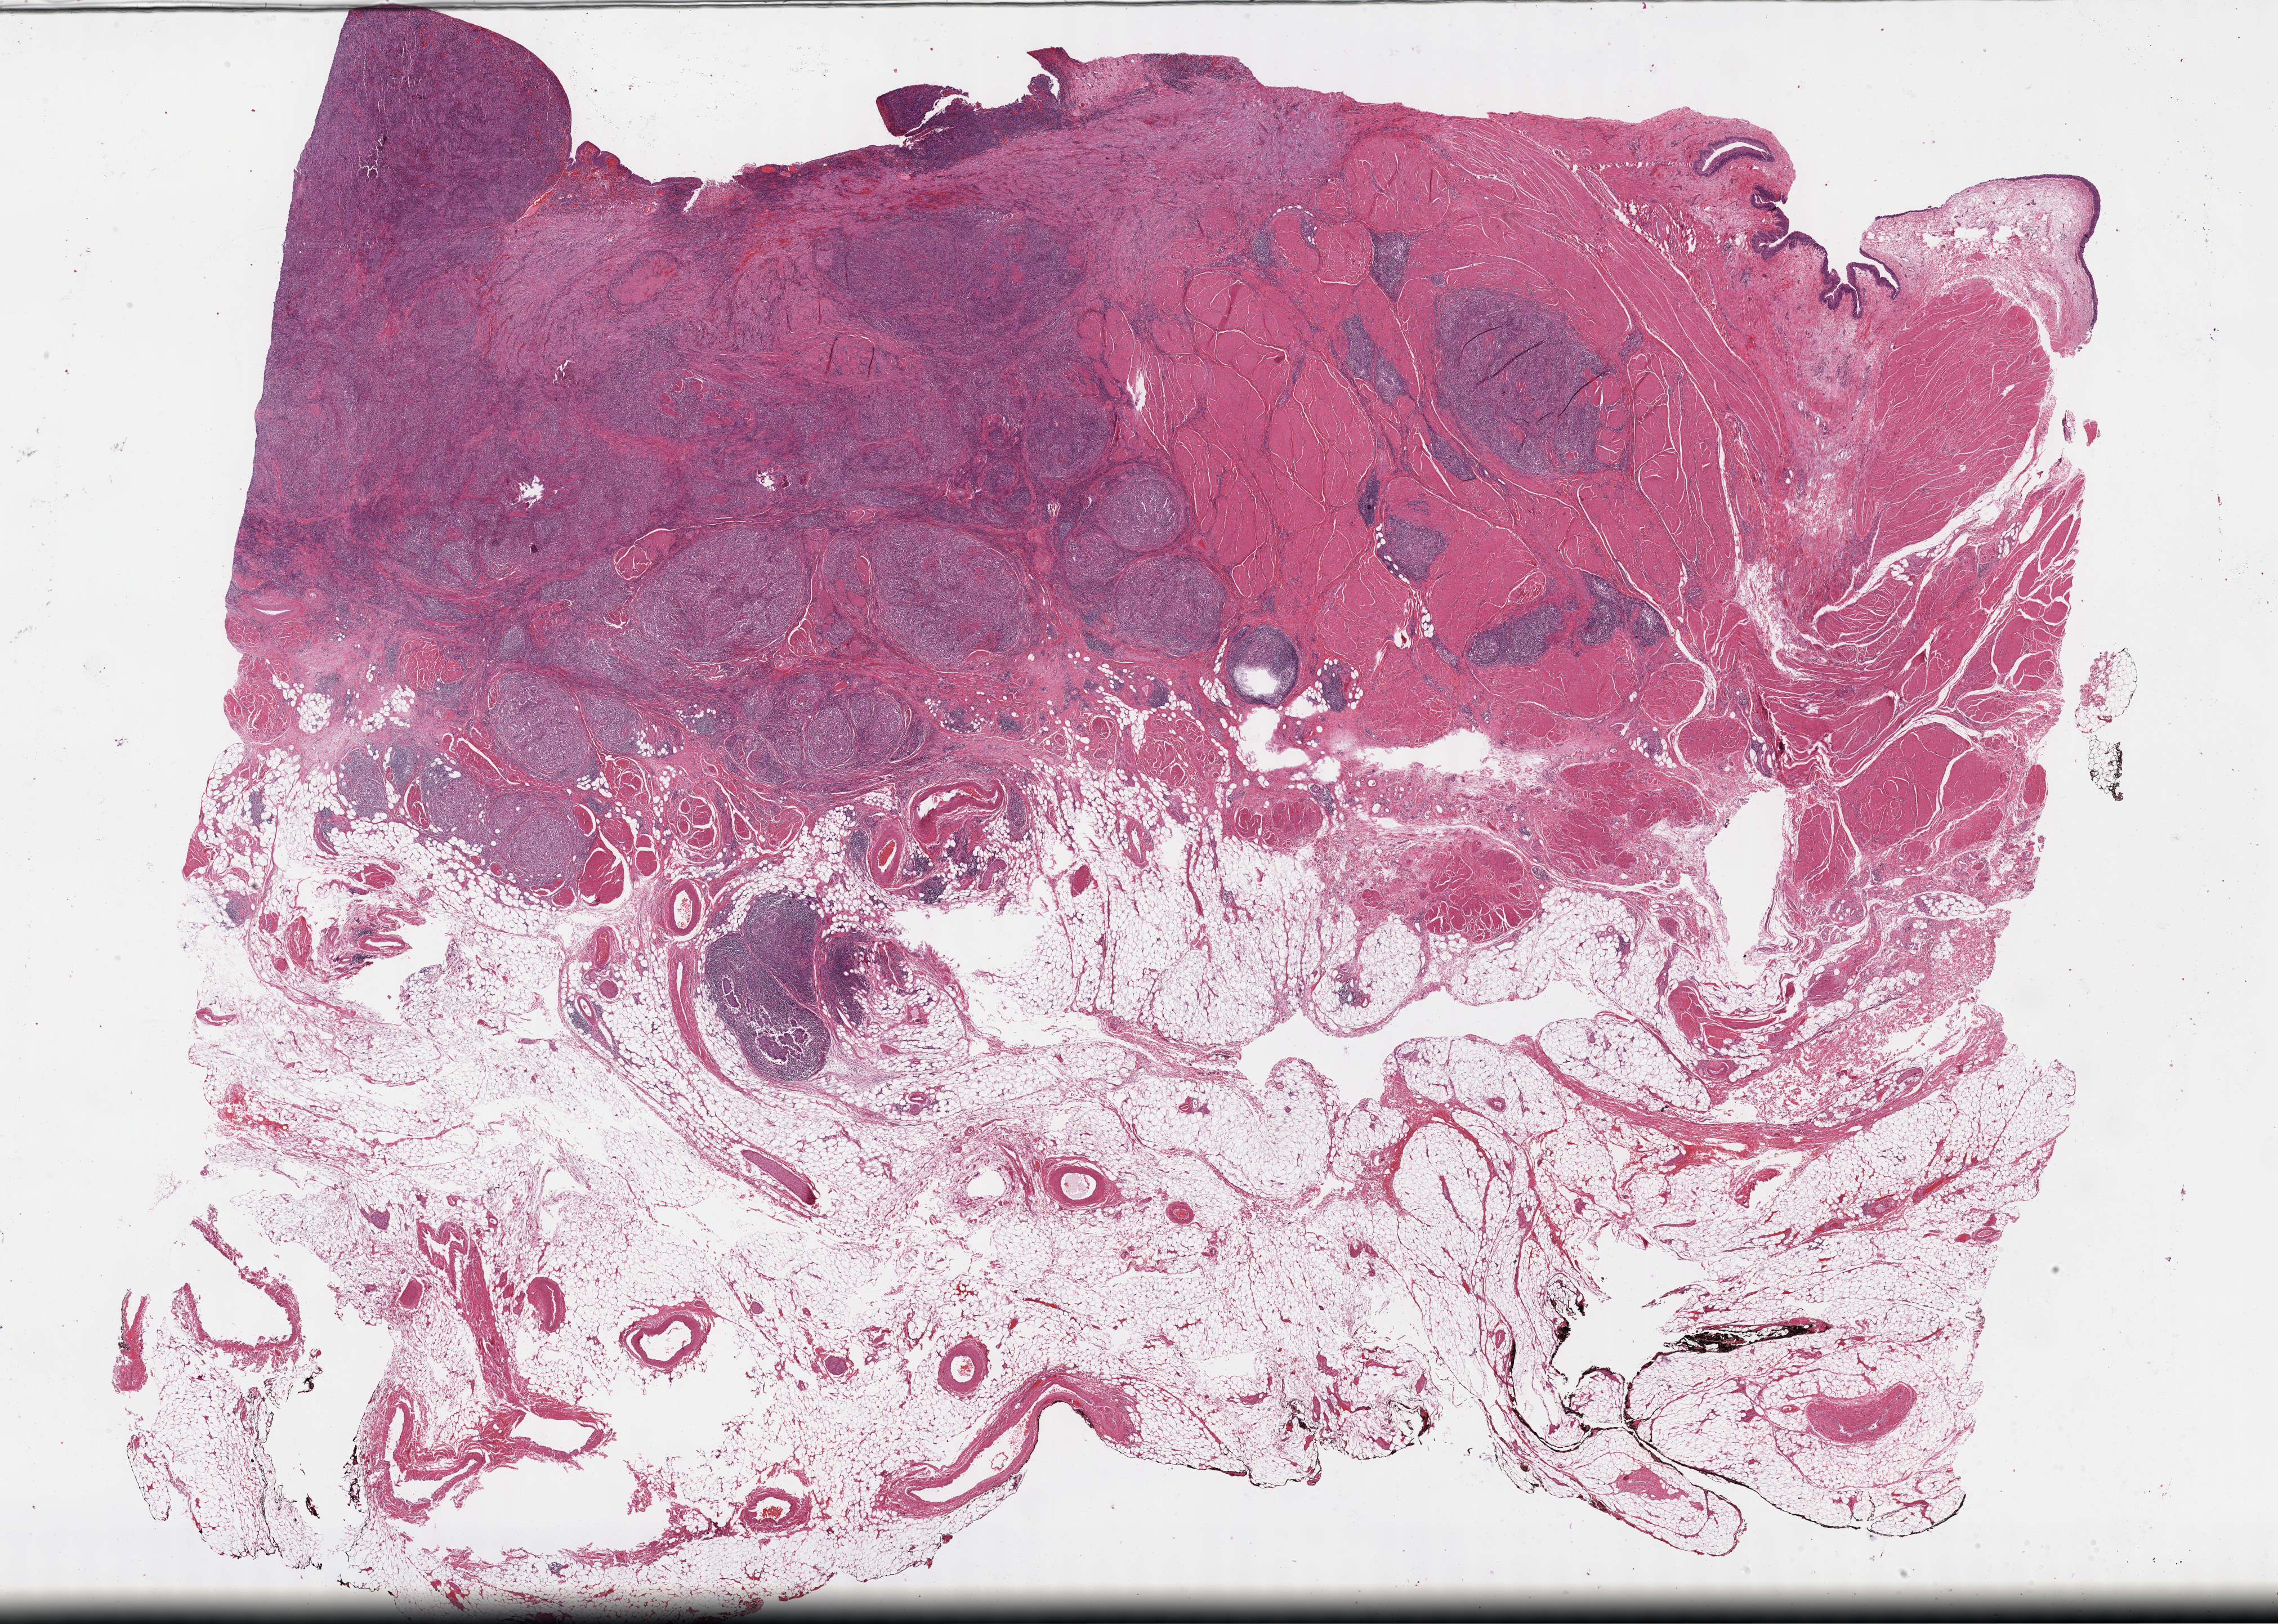
Digitized H&E tissue section (whole slide), a low-resolution overview of the entire scanned area, about 32.7 x 23.3 mm (acquisition: 40x scan), formalin-fixed paraffin-embedded (FFPE) diagnostic section, primary tumour sample from the bladder. Male patient; age at initial diagnosis 68 years. Histologic grade: high grade.
* AJCC pathologic stage: III (7th edition)
* pathologic diagnosis: Transitional cell carcinoma (posterior wall of bladder)
* lymph nodes positive (case pathology): 0 of 23 examined
* TNM: T3b N0 MX